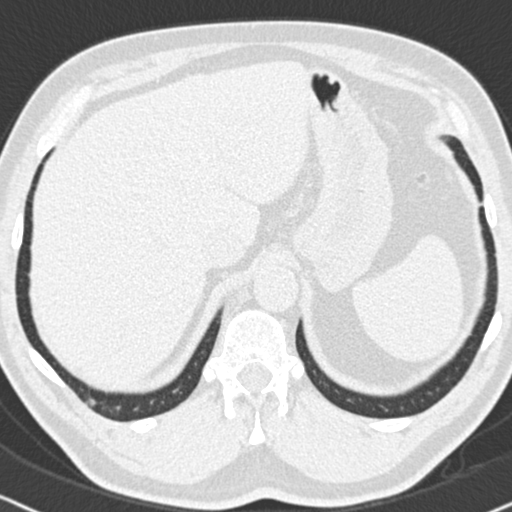
Low-dose screening chest CT, axial slice. Baseline screening round. Lung window (W 1500 / L -600 HU). 512 × 512 image matrix, field of view 325 × 325 mm. Male, age 63 years at enrolment. Former smoker at enrolment.
- Lesion marked by an expert reader, bounding box [x1, y1, x2, y2] px = [78, 386, 104, 416].
- No non-calcified nodule or mass ≥4 mm was recorded by the screening reader at this exam.
- Later outcome: lung cancer diagnosed 626 days after this screen (after the second annual screen) — adenocarcinoma, NOS, right lower lobe, moderately differentiated (G2), stage IIIB (AJCC 6th edition), 17 mm at pathology.